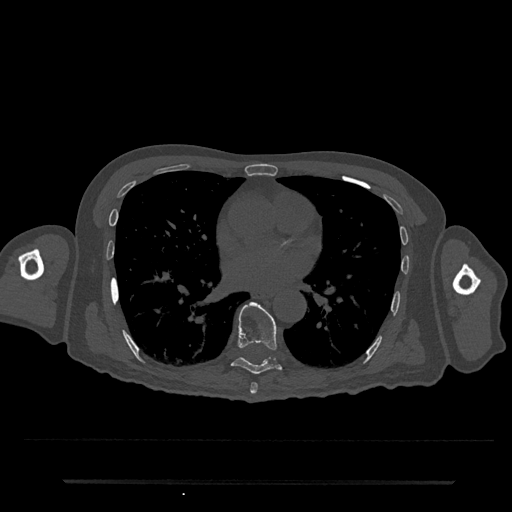
CT including the spine, one axial slice. Position 422 of 797 along the scan axis. Reconstruction kernel Br40s/3. 120 kVp. Bone window (W 1800 / L 400 HU). 512 × 512 image matrix. Patient: male, 74 years. Case-level facts recorded for this patient, not image findings: primary cancer: prostate.
Outlined on this slice (semi-automatically segmented with operator editing):
- T7 vertebra: bounding box [x1, y1, x2, y2] px = [250, 383, 258, 394]
- T8 vertebra: [231, 302, 282, 374]